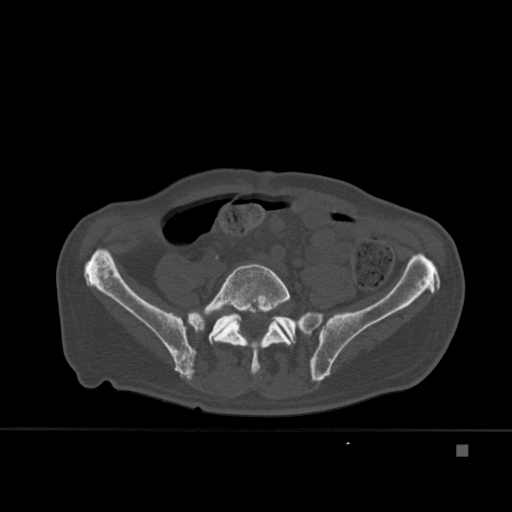
CT including the spine, one axial slice; position 100 of 451 along the scan axis; bone window (W 1800 / L 400 HU); 1.5 mm slice thickness; 512 × 512 image matrix, field of view 378 × 378 mm. Male patient, age 75 years. Case-level facts recorded for this patient, not image findings: primary cancer: prostate.
Annotated regions visible in this slice (semi-automatically segmented with operator editing):
- L5 vertebra: bounding box [x1, y1, x2, y2] px = [187, 263, 292, 375]
- T7 vertebra: [215, 298, 246, 339]